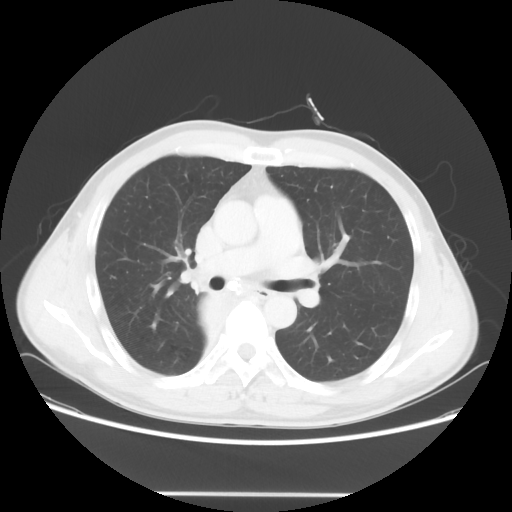
Chest CT, one axial slice. Position 37 of 62 along the scan axis. Lung window (W 1500 / L -600 HU). 5 mm slice thickness. 512 × 512 image matrix, field of view 393 × 393 mm. Male patient, age 47 years. Case-level facts recorded for this patient, not image findings: clinical TNM (as recorded): T2 N0 M0.
Structures marked on this image (rectangle marked by the reading radiologist):
- lung tumour (recorded histology: squamous cell carcinoma): bounding box (x1, y1, x2, y2) in pixels: (190, 286, 245, 342)